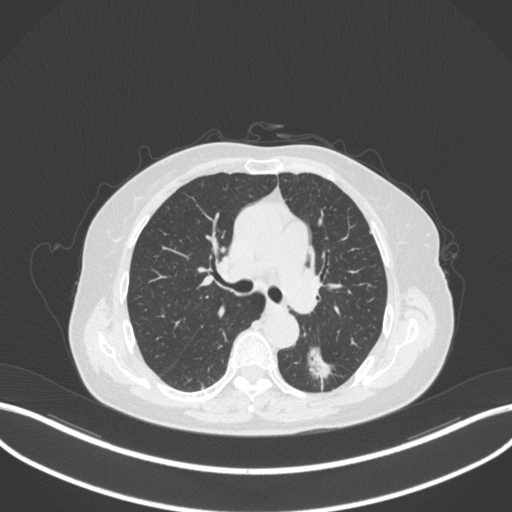
Chest CT, one axial slice. Slice 185 of 352 in the series (ordered by position). Reconstruction kernel B31f. 120 kVp. Lung window (W 1500 / L -600 HU). 1 mm slice thickness. 512 × 512 image matrix, field of view 400 × 400 mm. Patient: female, 70 years. Case-level facts recorded for this patient, not image findings: clinical TNM (as recorded): T1c N0 M0.
Annotated regions visible in this slice (bounding box drawn by a radiologist):
- lung tumour (recorded histology: adenocarcinoma): box from (x=300, y=341) to (x=340, y=386) px